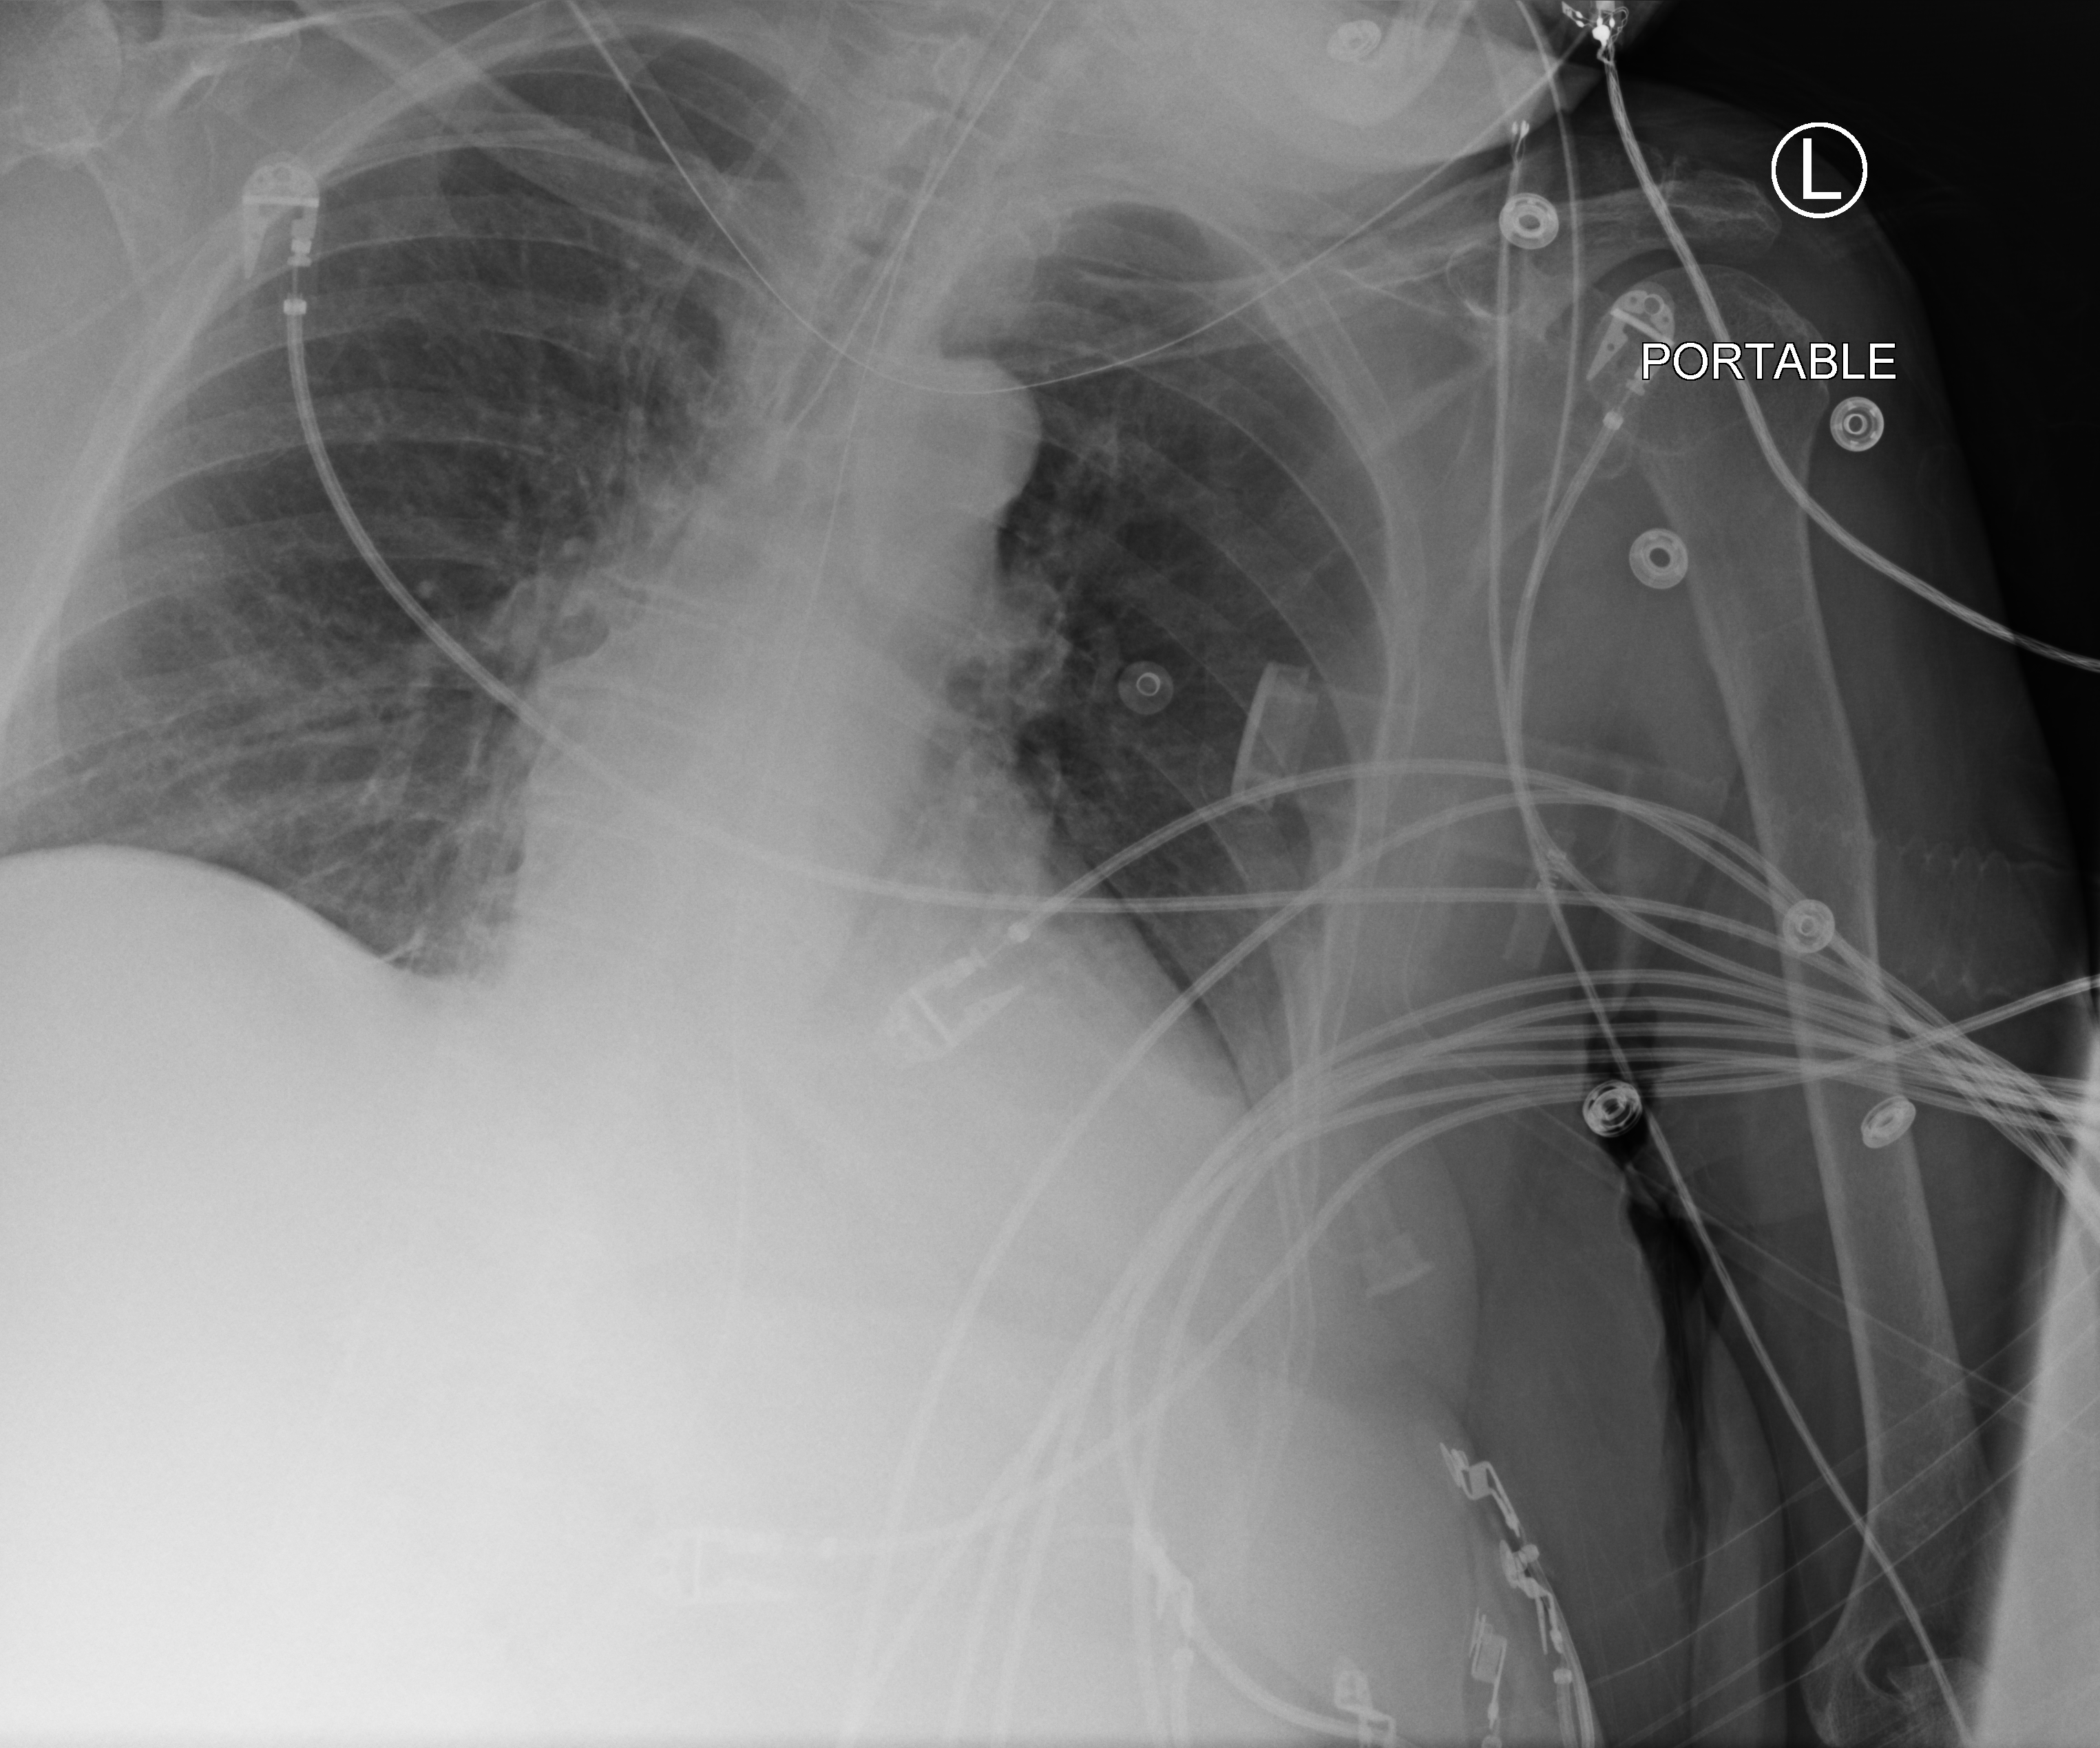
Bedside chest radiograph (computed radiography). Female patient hospitalised with COVID-19, age 75–90 years.
From the hospital-stay record, not from the radiograph (when in the stay this image was taken is not recorded): mechanically ventilated during this hospital stay: yes.